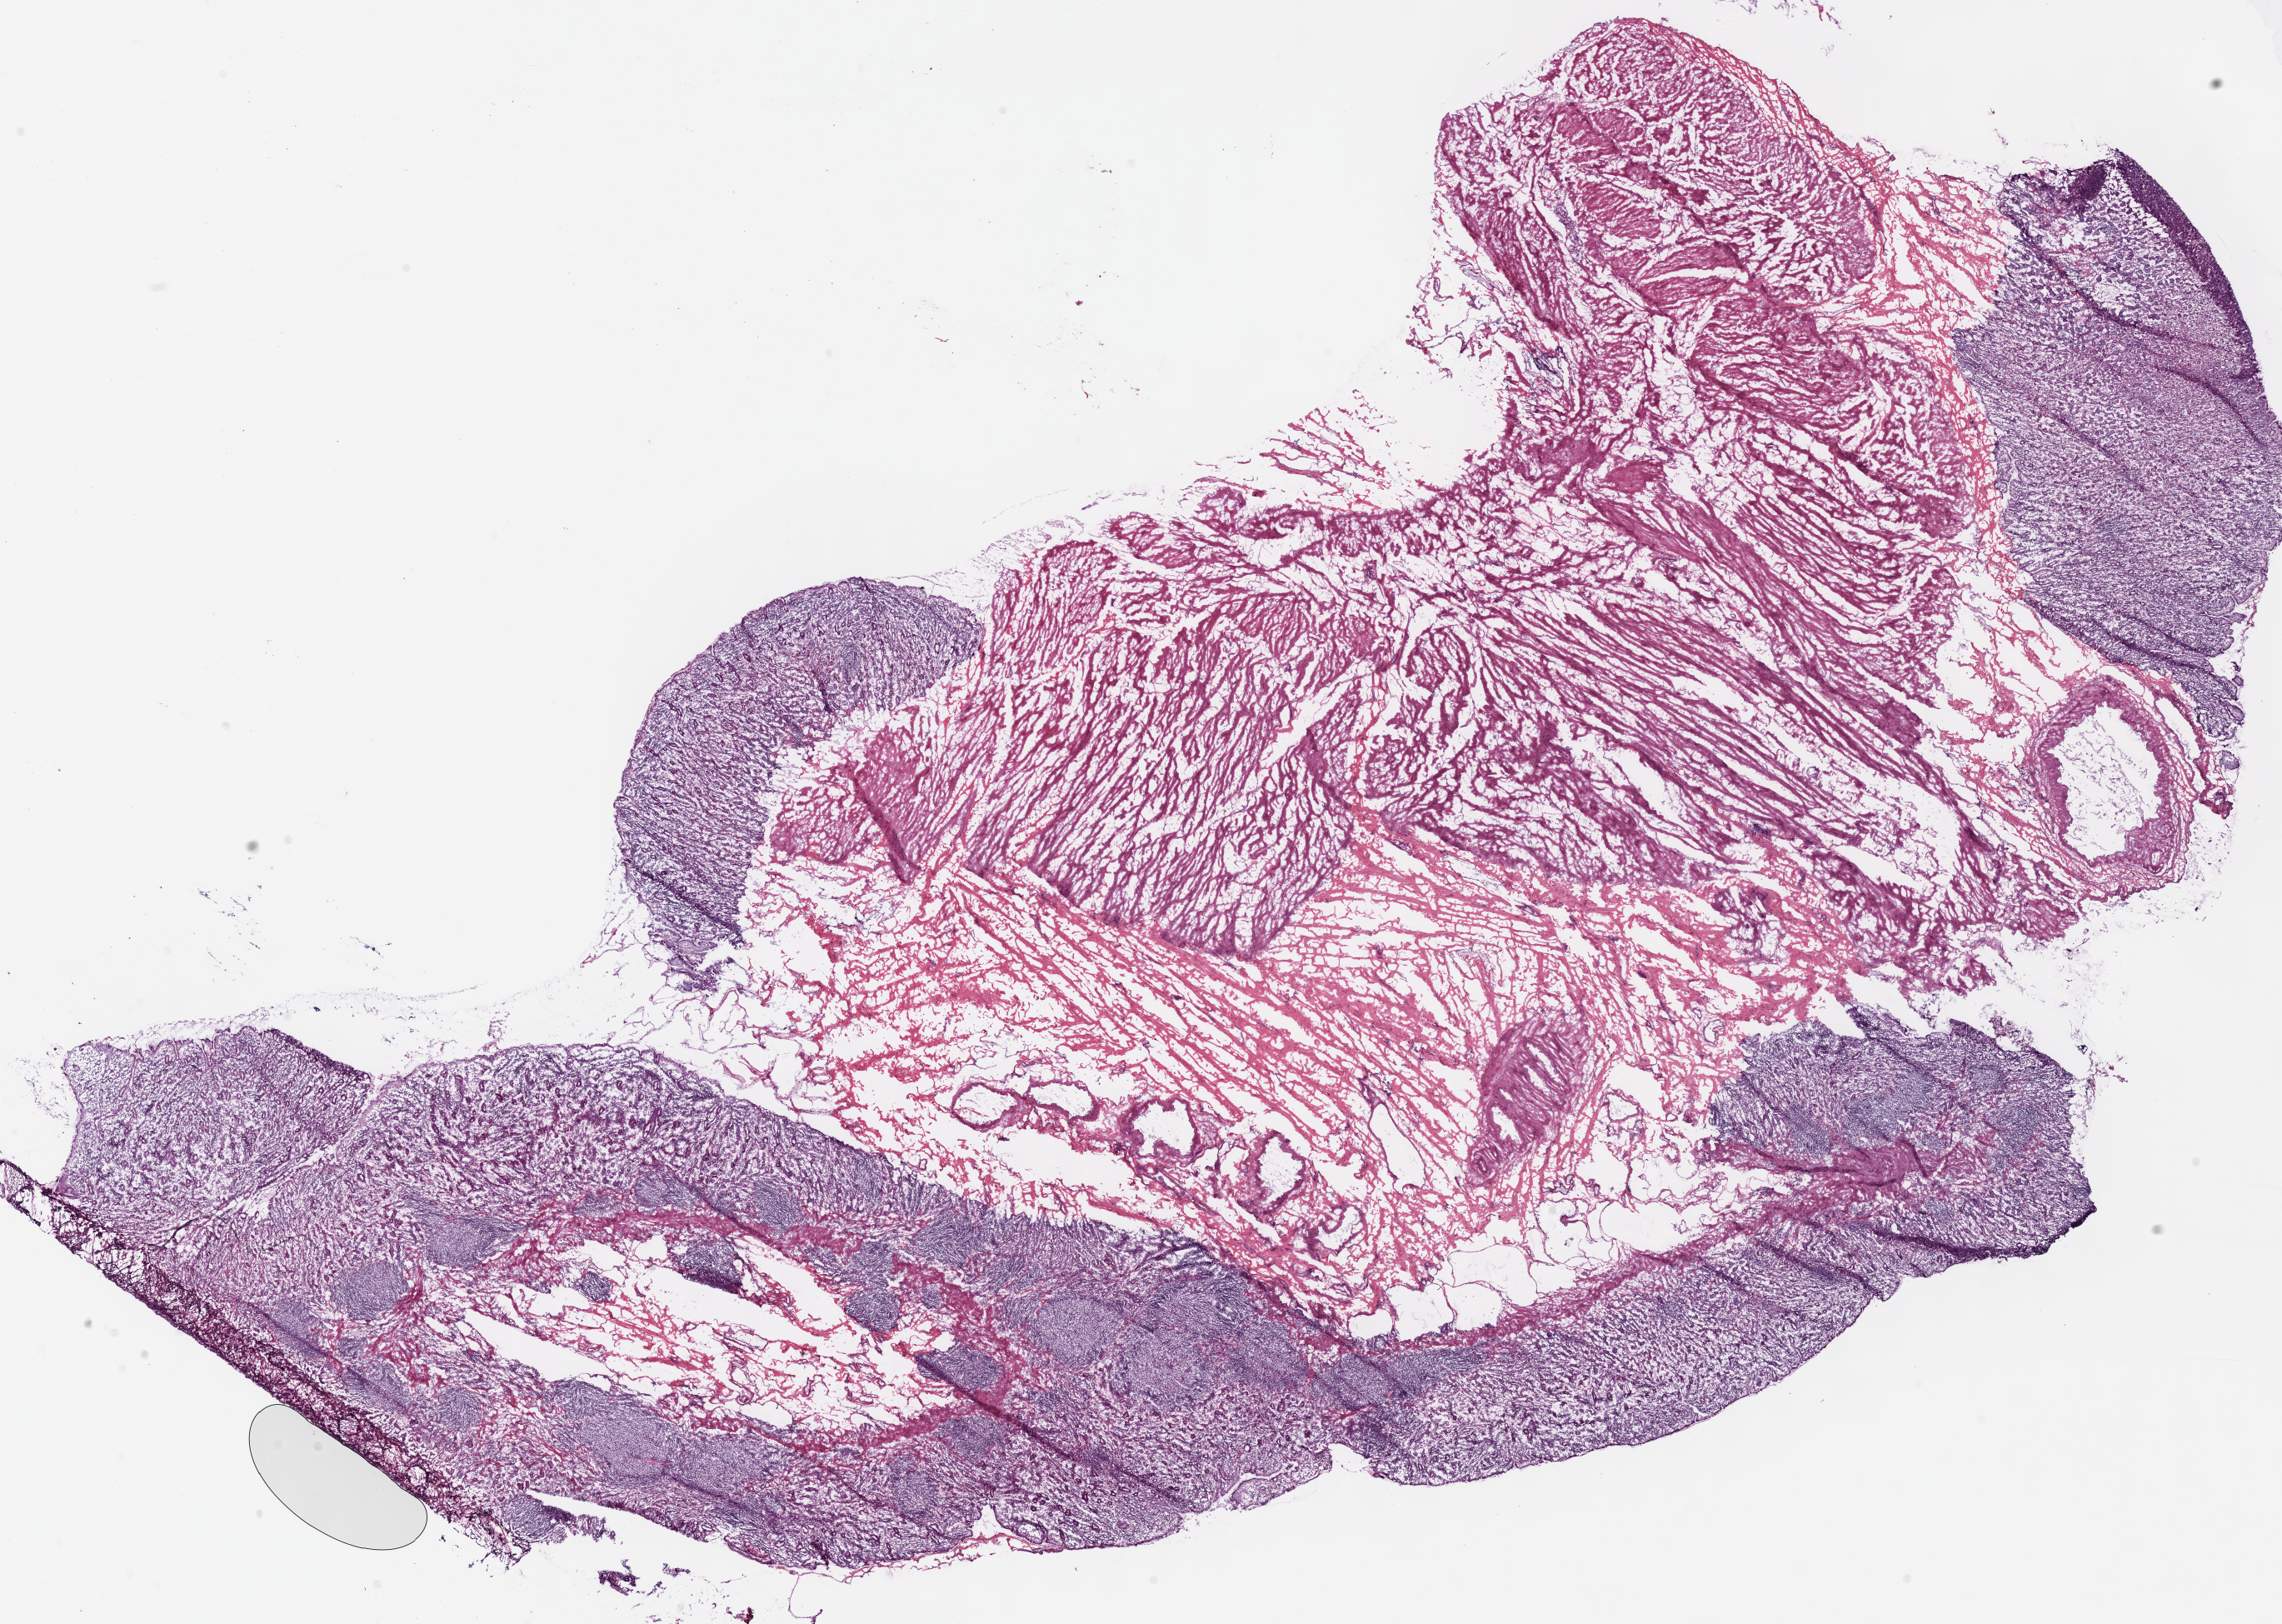
Digitized H&E-stained tissue section (whole slide) — a low-resolution overview of the entire scanned area, about 21.5 x 15.3 mm. Frozen section from the top of the tissue portion. Sample: solid tissue normal (non-tumour tissue), stomach. Male, age 63 years at initial diagnosis. Inflammatory infiltration, as recorded: lymphocyte infiltration 50%, monocyte infiltration 0%, neutrophil infiltration 5%.
This section: solid tissue normal (non-tumour) sample from the same patient. Patient diagnosis: Adenocarcinoma, NOS.